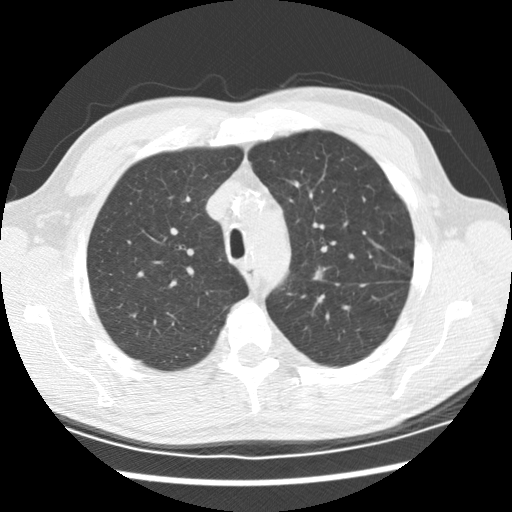
Low-dose screening chest CT, one axial slice. Position 155 of 208 along the scan axis. 120 kVp. Lung window (W 1500 / L -600 HU). 512 × 512 image matrix.
Annotated regions visible in this slice (expert manual segmentation):
- lesion 1 (tumor, upper lobe of left lung): box from (x=312, y=270) to (x=324, y=280) px